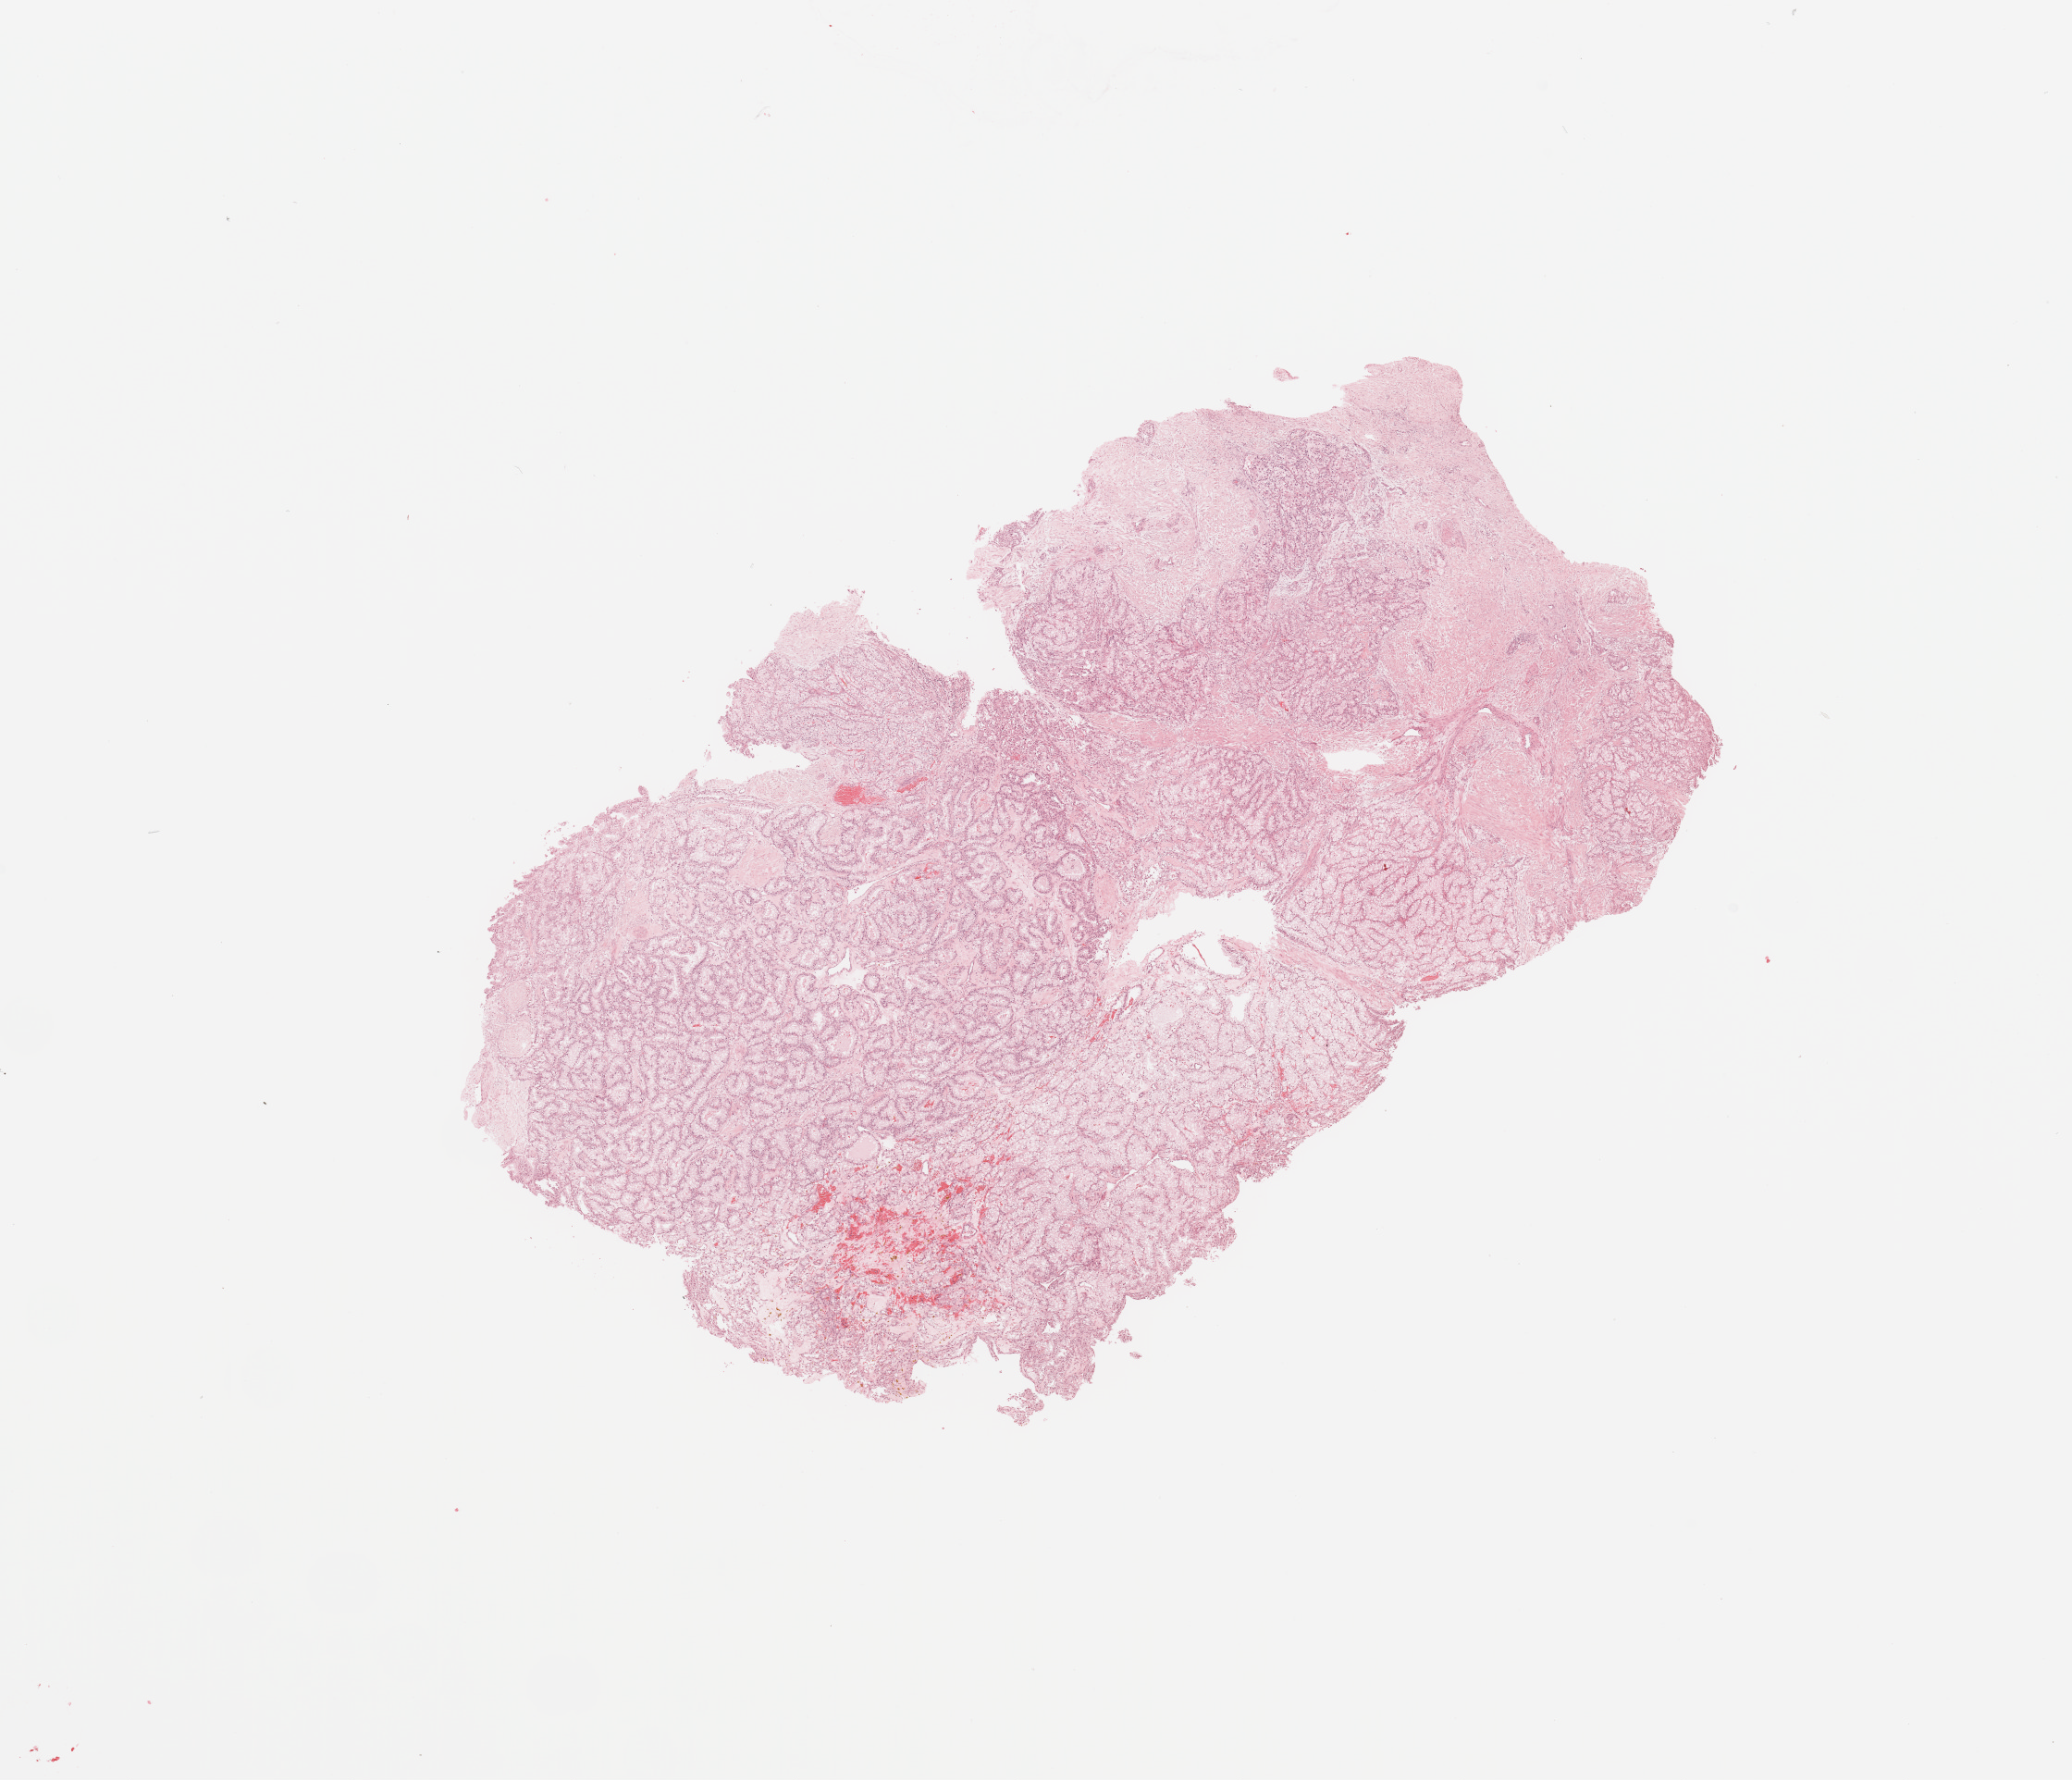
Digitized Hematoxylin and eosin (H&E) stained tissue section (whole slide), whole scanned area (about 17.7 x 15.2 mm, acquisition: 20x scan) shown as a low-resolution overview. Tumour tissue sample, sampled site: kidney. Female, 66 y/o. Histologic grade: G2 (moderately differentiated). Composition of this section per pathologist review: tumour nuclei 85%, necrosis 3%.
Histologic diagnosis: Renal cell carcinoma, NOS. AJCC pathologic stage: I.